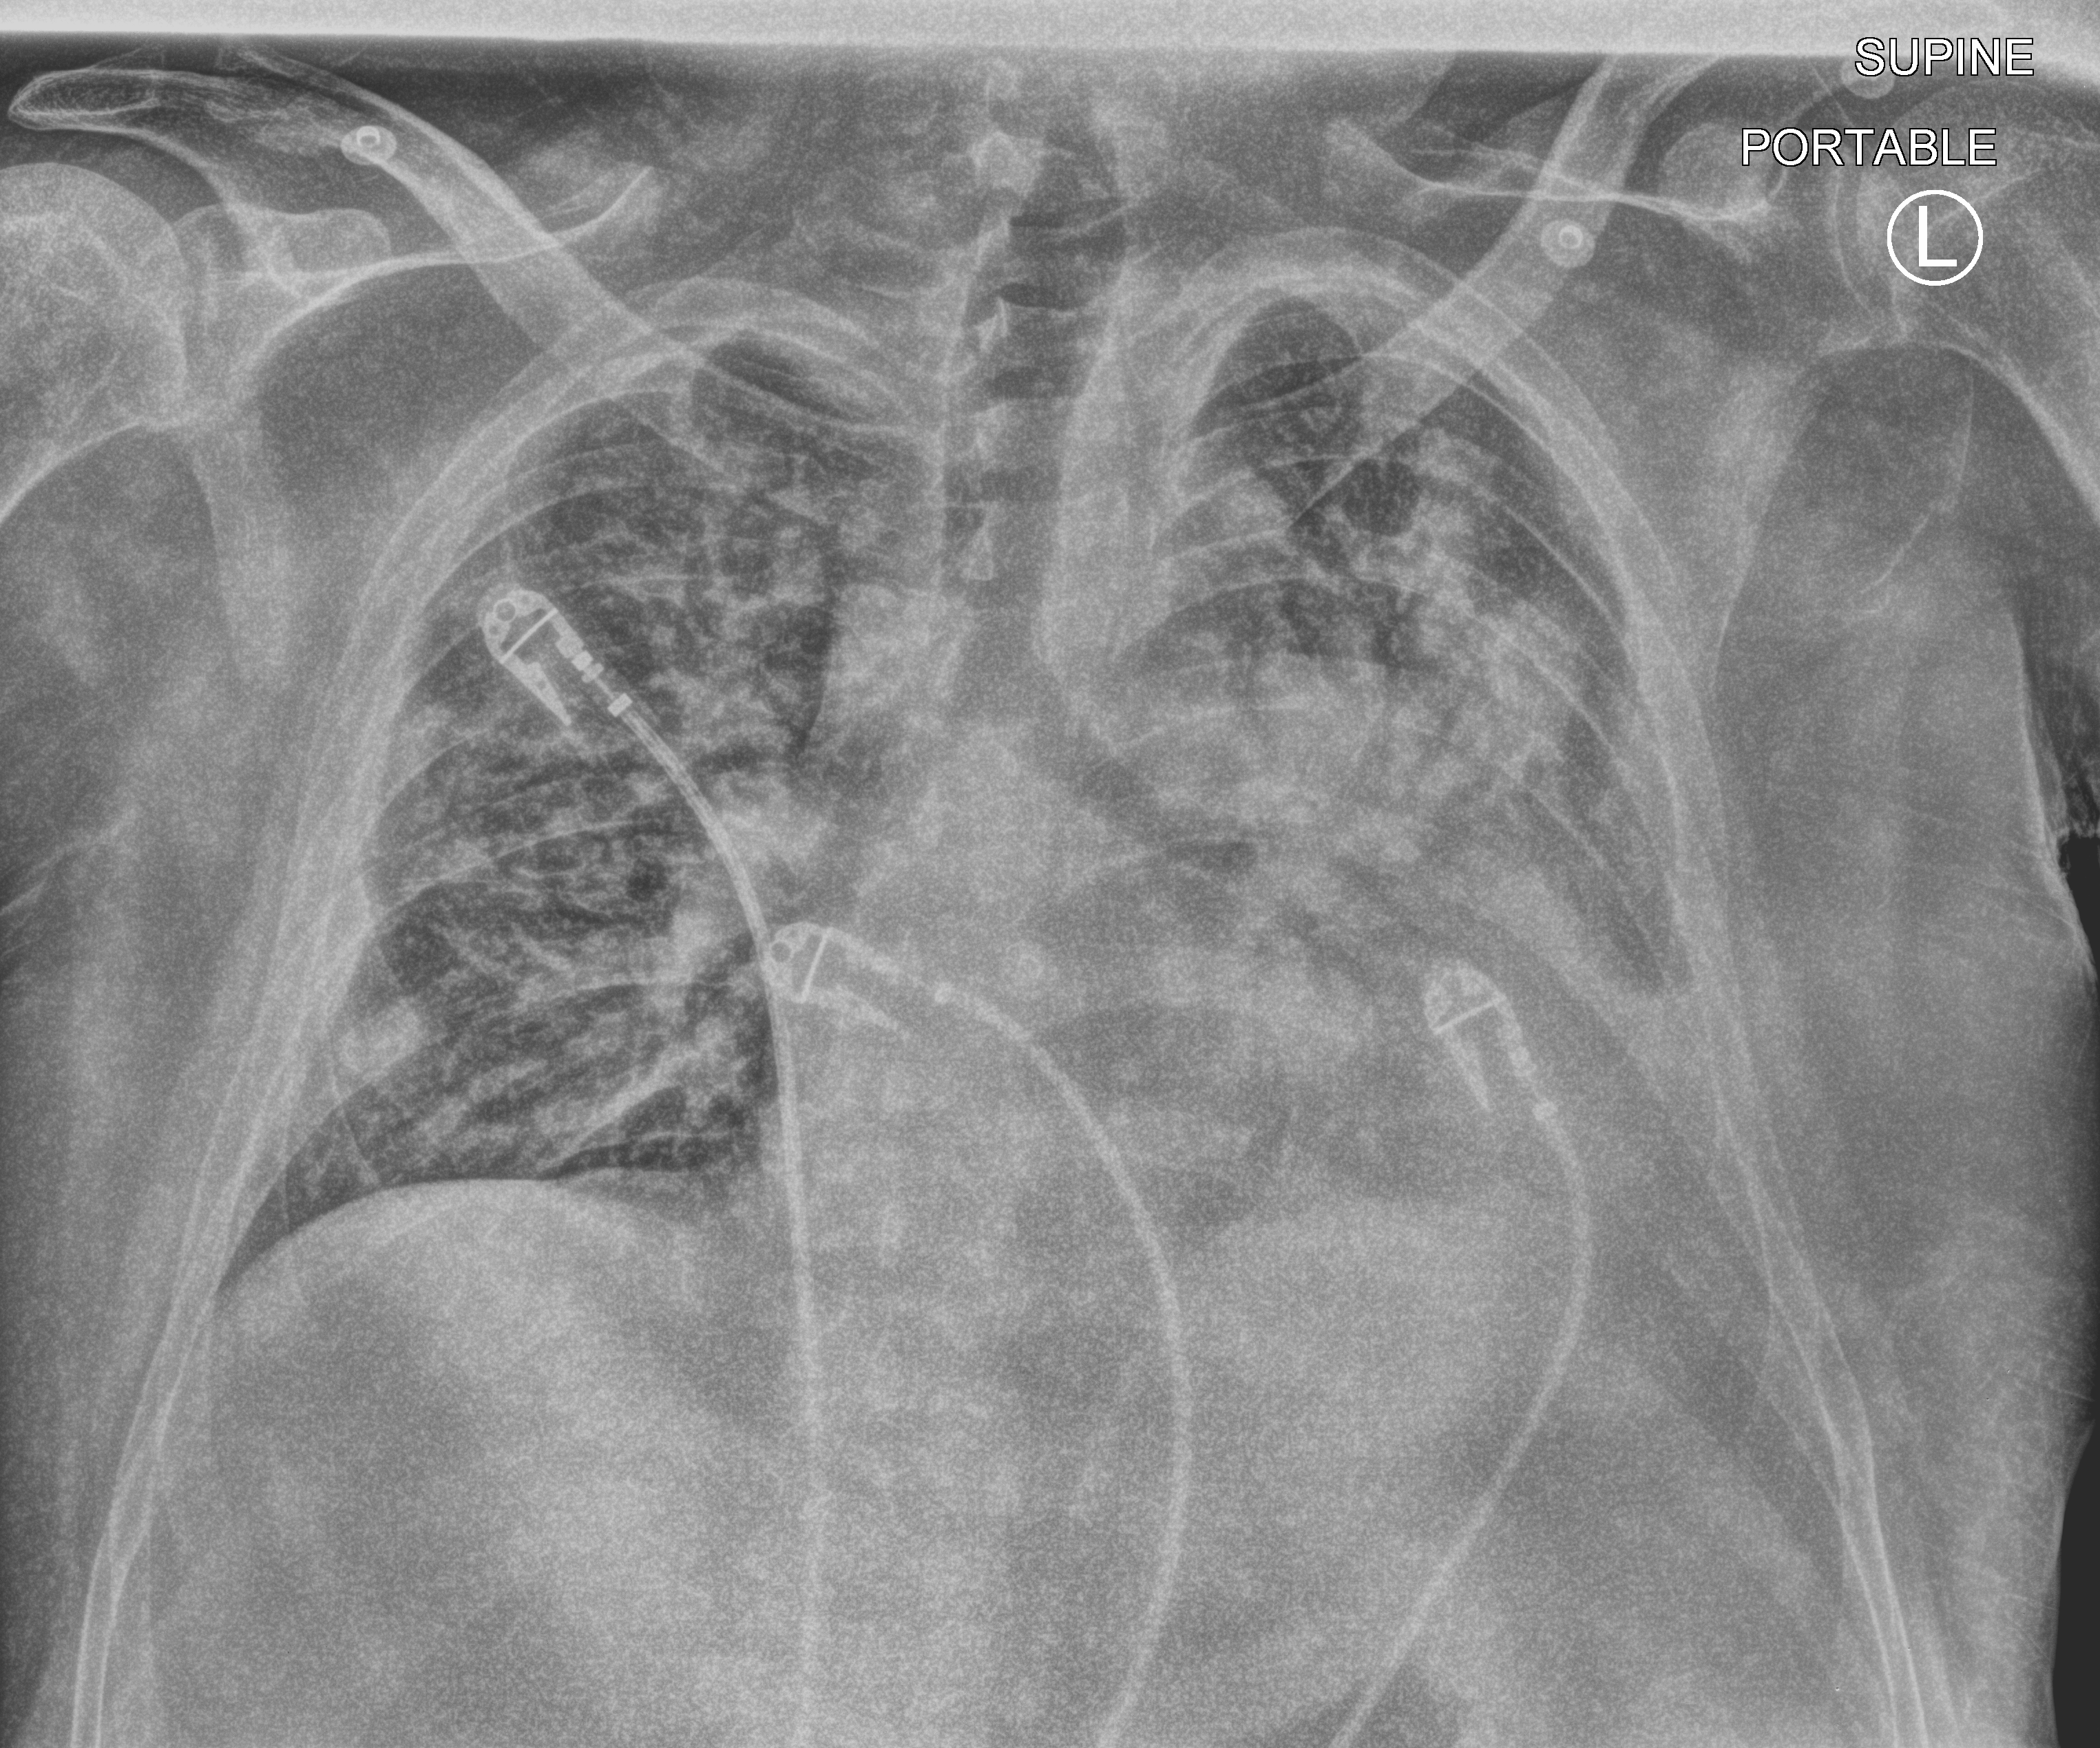
Chest X-ray (portable), anteroposterior (AP) projection. Male patient hospitalised with COVID-19, age 18–59 years.
Admission-level facts for this patient (not findings on this image; timing relative to this image not recorded): length of hospital stay: 15 days.